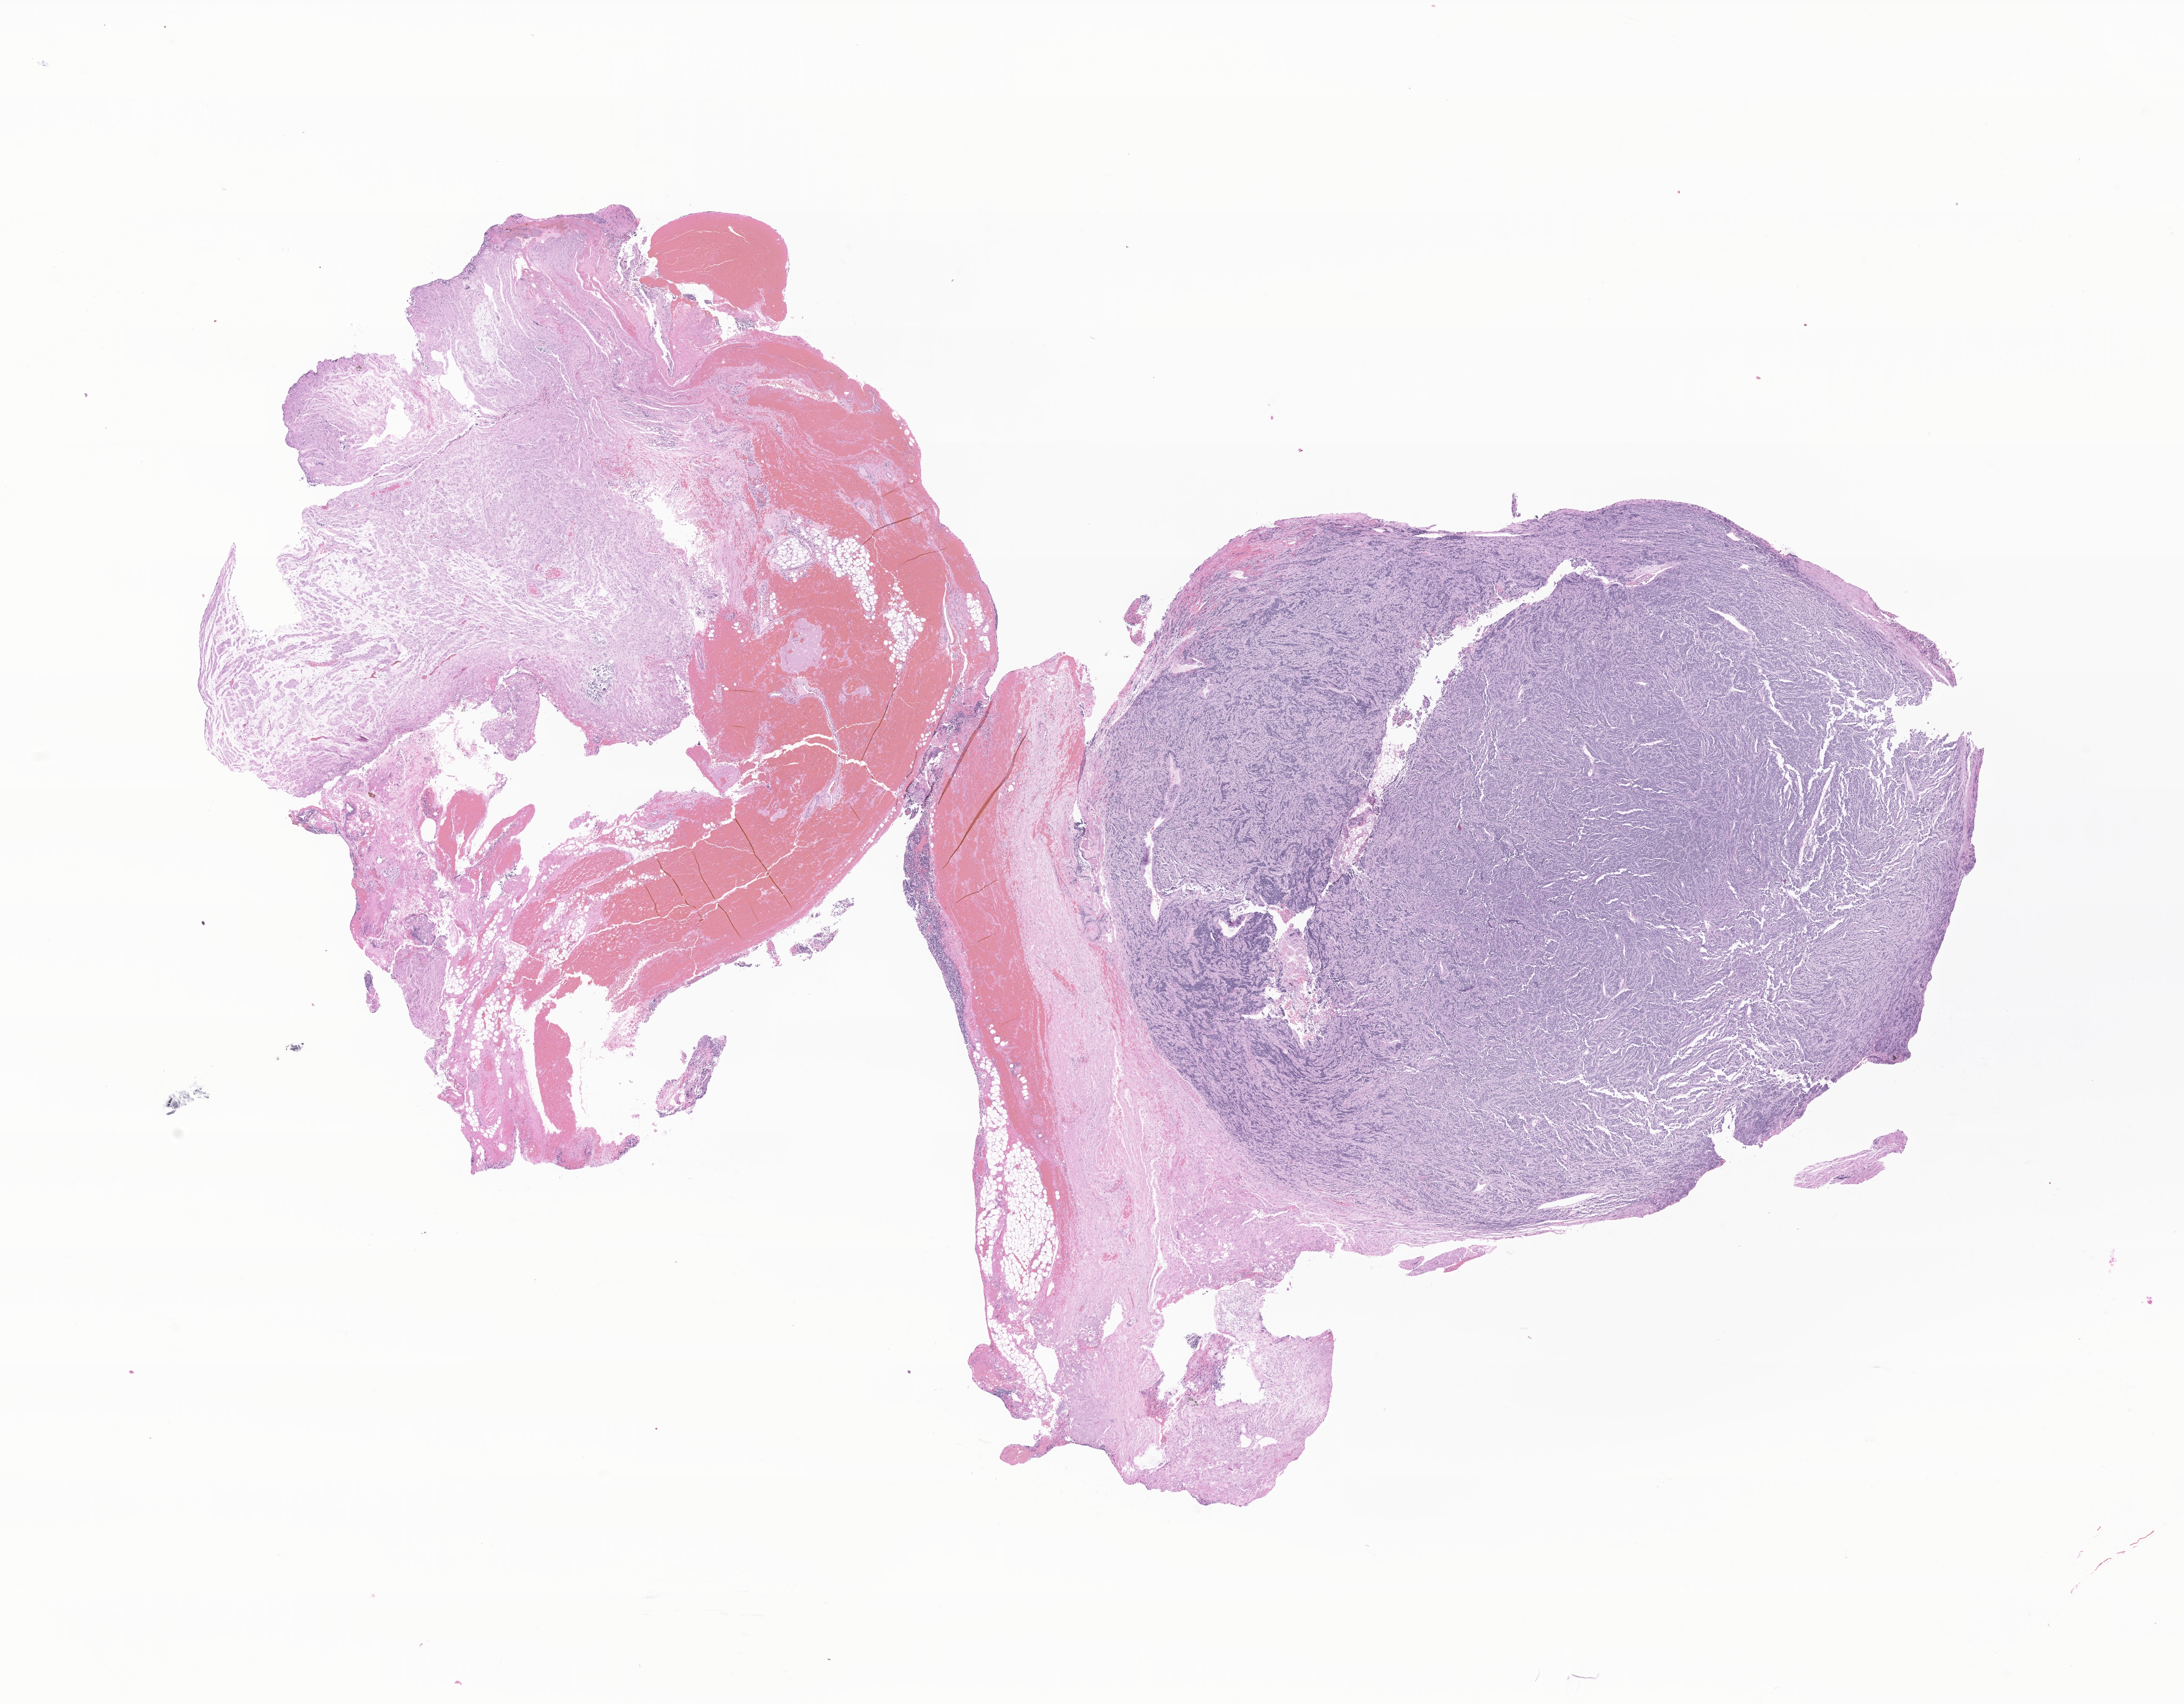
Digitized H&E-stained section of tumor tissue from the adrenal gland, whole scanned area (about 20.3 x 15.8 mm) shown as a low-resolution overview. FFPE section. Patient female; age 89 months (7 years 5 months).
Diagnosis: Ganglioneuroblastoma.